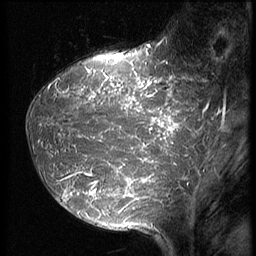
Breast MRI (dynamic contrast-enhanced), one sagittal slice. Position 19 of 64 along the scan axis. 3 images stored at this slice position (order not interpretable as contrast timing). 1.5 T. TE 4.2 ms, TR 9 ms. 2.5 mm slice thickness. 256 × 256 image matrix. Patient: female, 39 years. Case-level facts recorded for this patient, not image findings: setting: breast cancer imaged before/during neoadjuvant chemotherapy; receptor status: HER2-positive.
Outlined on this slice (semi-automatically segmented with operator editing):
- analysis volume of interest (the breast-tissue region the enhancement analysis was run in; not a lesion): bounding box (x1, y1, x2, y2) in pixels: (26, 47, 210, 239)
- tumour enhancement mask (voxels above the 140 % enhancement threshold inside the analysis volume of interest): (56, 47, 205, 214)